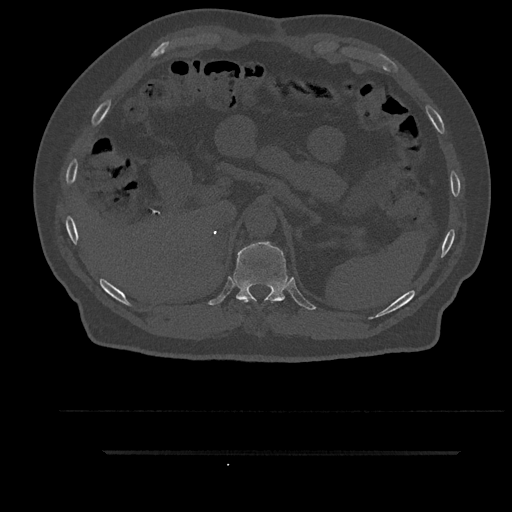
CT including the spine, one axial slice; position 325 of 797 along the scan axis; reconstruction kernel Br40s/3; 120 kVp; bone window (W 1800 / L 400 HU); 0.5 mm slice thickness; 512 × 512 image matrix, field of view 432 × 432 mm. Patient: male, 63 years. Case-level facts recorded for this patient, not image findings: primary cancer: renal; vertebrae with lytic lesions (as recorded): T8.
Outlined on this slice (semi-automatic segmentation, software-assisted and operator-edited):
- T10 vertebra: bounding box <246,300,273,303> (left, top, right, bottom; pixels)
- T11 vertebra: <233,242,288,302>